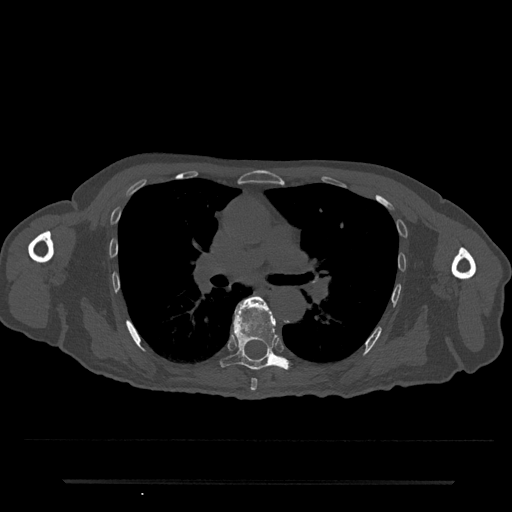
CT including the spine, one axial slice; position 490 of 797 along the scan axis; reconstruction kernel Br40s/3; 120 kVp; bone window (W 1800 / L 400 HU); 512 × 512 image matrix, field of view 427 × 427 mm. Patient: male, 74 years. Case-level facts recorded for this patient, not image findings: primary cancer: prostate.
Structures marked on this image (semi-automatically segmented with operator editing):
- T6 vertebra: bounding box <246,297,263,391> (left, top, right, bottom; pixels)
- T7 vertebra: <220,298,291,370>